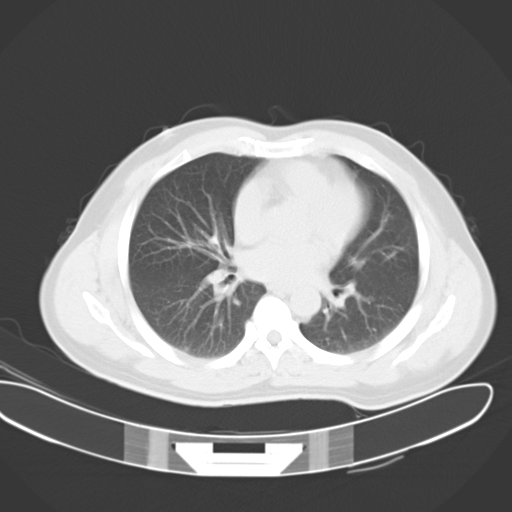
Chest CT, one axial slice. Slice 12 of 24 in the series (ordered by position). Reconstruction kernel B40f. 120 kVp. Lung window (W 1500 / L -600 HU). 10 mm slice thickness. 512 × 512 image matrix. Male patient, age 54 years. From the clinical record (not read from this slice): clinical TNM (as recorded): Tis N0 M0.
Outlined on this slice (rectangle marked by the reading radiologist):
- lung tumour (recorded histology: adenocarcinoma): bounding box (x1, y1, x2, y2) in pixels: (177, 341, 198, 356)